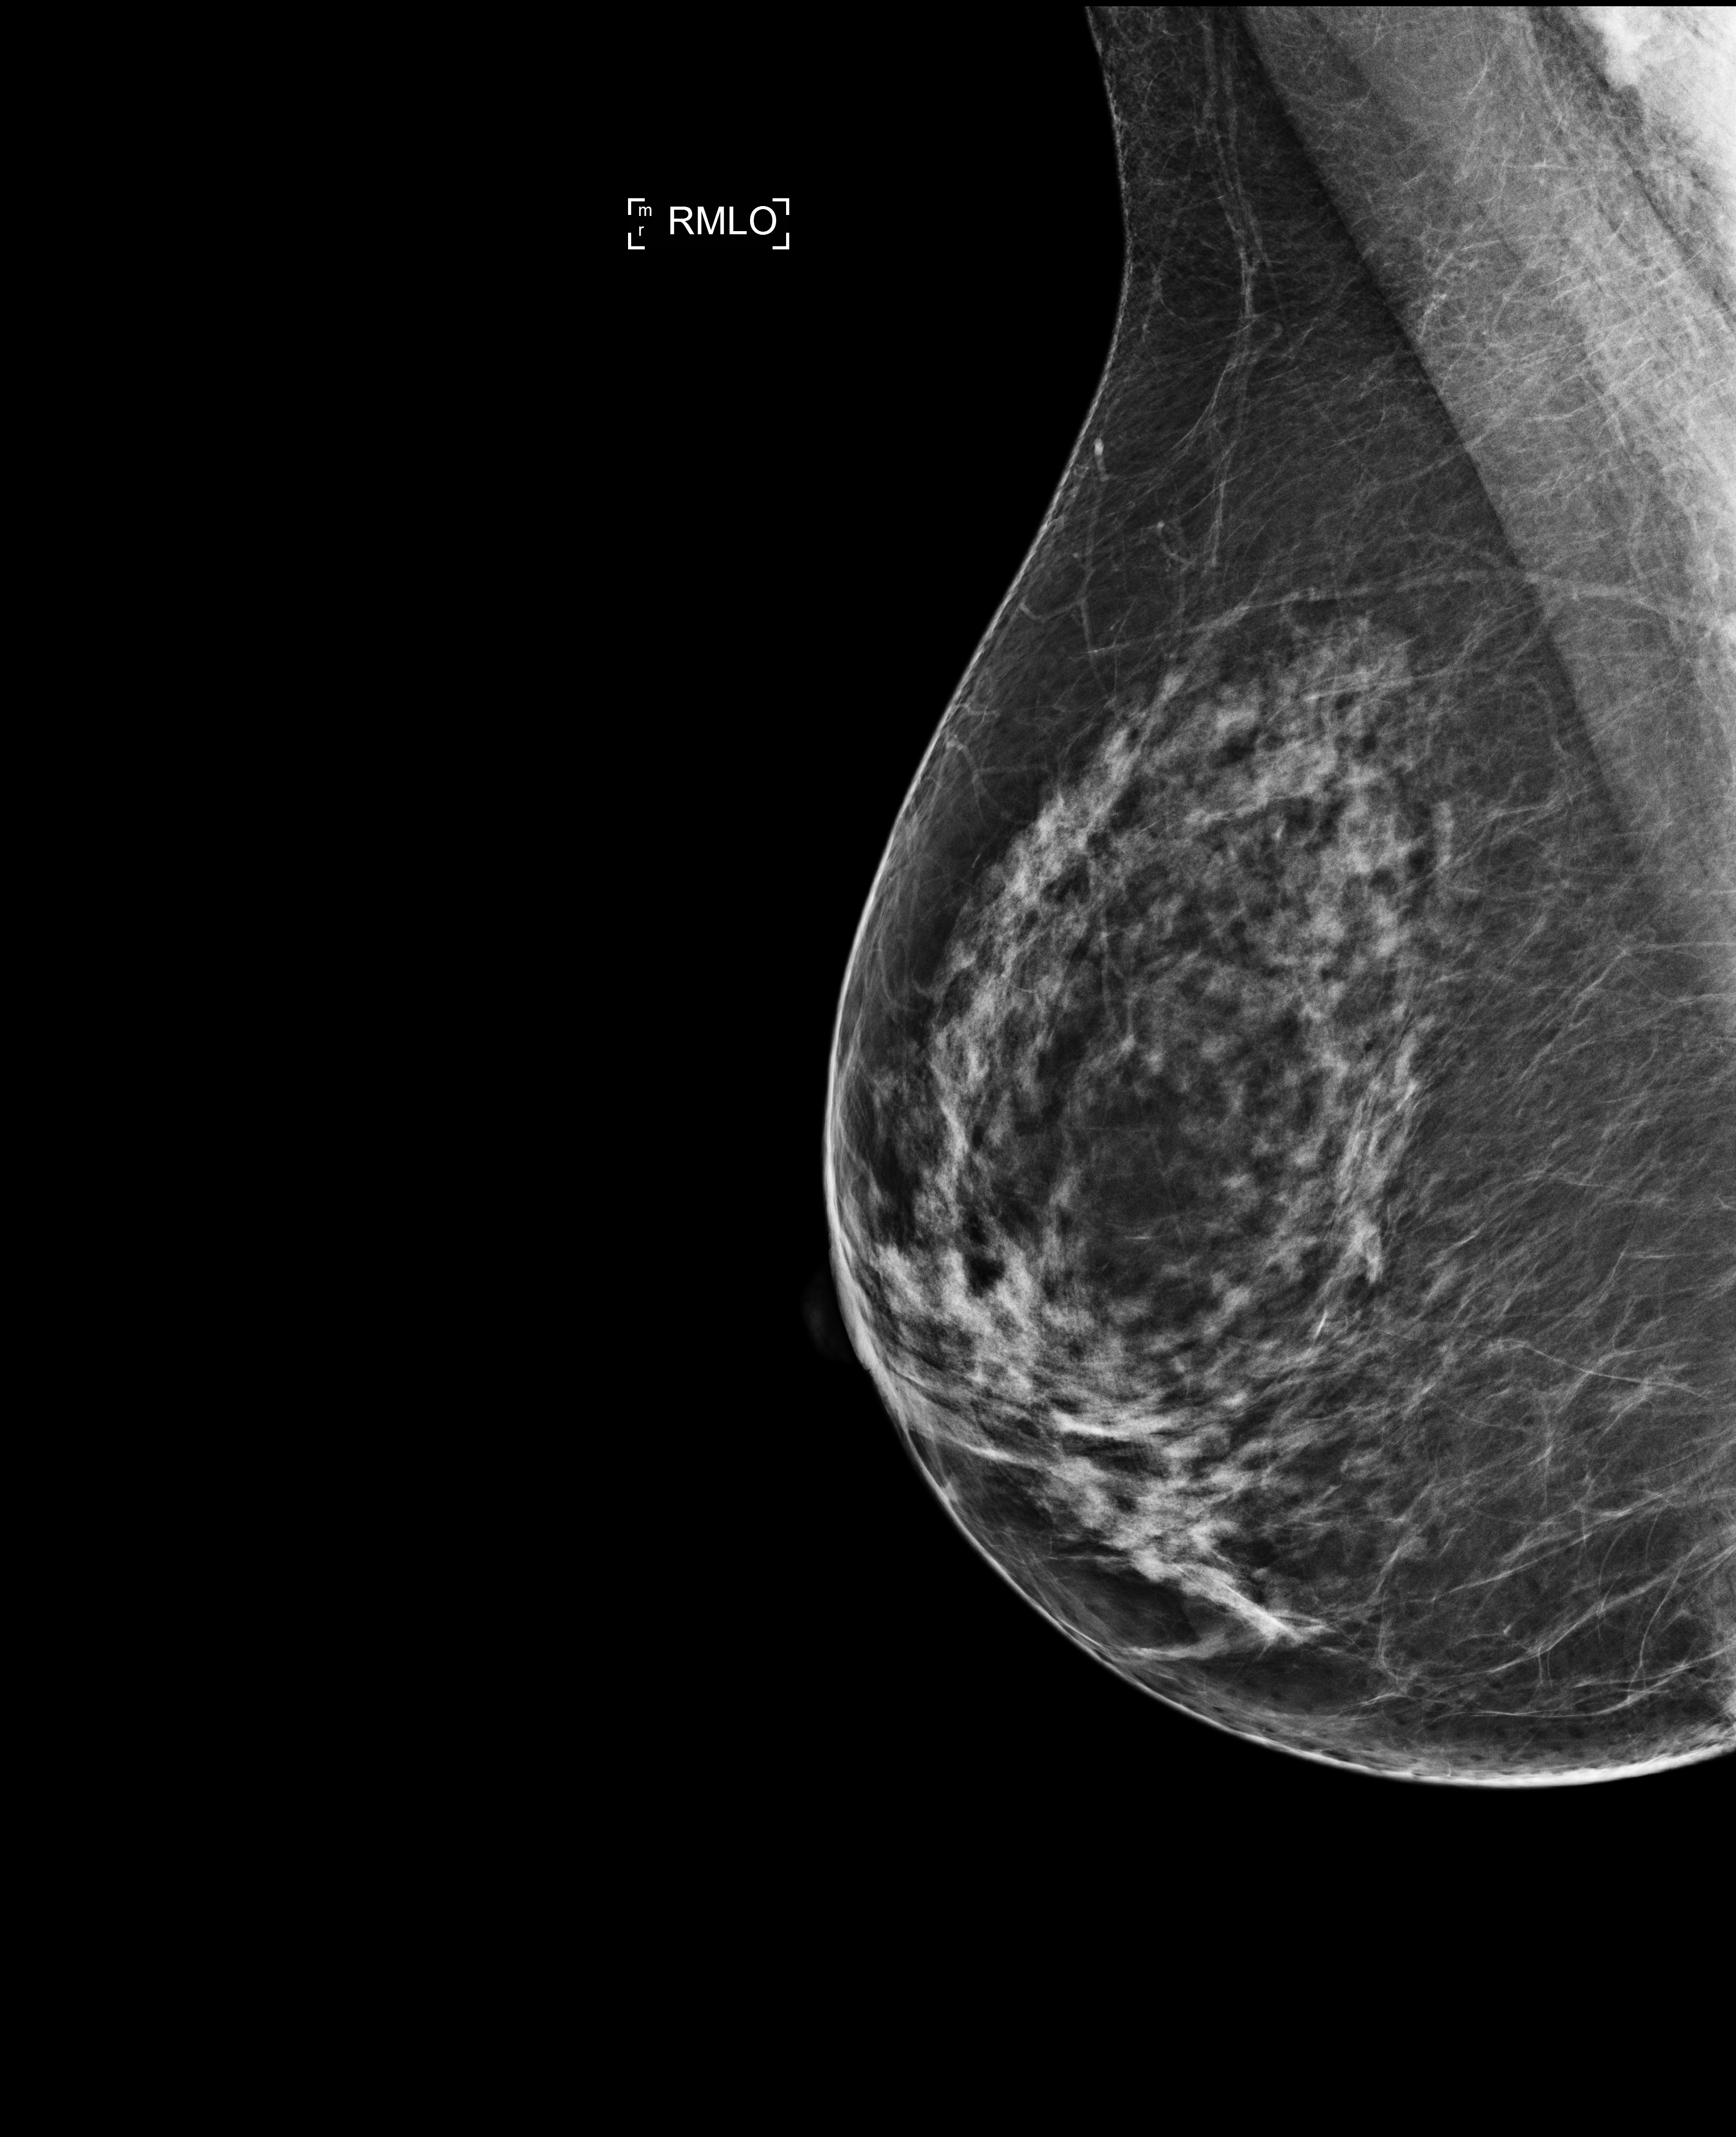
Screening examination; compressed breast thickness 71 mm; system: Selenia Dimensions. Patient: female, 53 years.
Image type: full-field digital mammogram. Breast: right. Projection: mediolateral oblique (MLO) view.